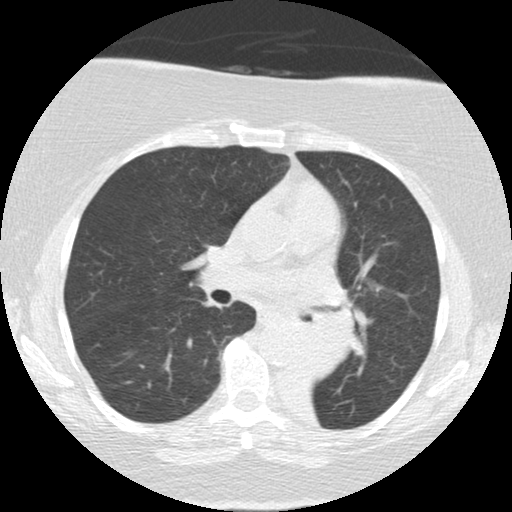
Chest CT (low-dose screening protocol), one axial image. First (baseline) screen. Lung window (W 1500 / L -600 HU). 2.5 mm slice thickness. 120 kVp. Slice 60 of 136 in the series. Female participant, aged 71 years at enrolment. Former smoker at enrolment.
Expert reader's lesion annotation, bounding box [x1, y1, x2, y2] px = [287, 307, 363, 383]. The exam's reader record, not a measurement of the box and not confirmed to be the same lesion: non-calcified nodule or mass ≥4 mm, right middle lobe, 5 × 5 mm, smooth margins, soft tissue attenuation. Note: the box lies in the patient's left hemithorax on this image, whereas the reader's record names the right lung; they may be different findings. Lung cancer was diagnosed 46 days after this screen: large cell carcinoma, NOS, left lower lobe, mediastinum, other location, poorly differentiated (G3), stage IV (AJCC 6th edition), 50 mm at pathology.